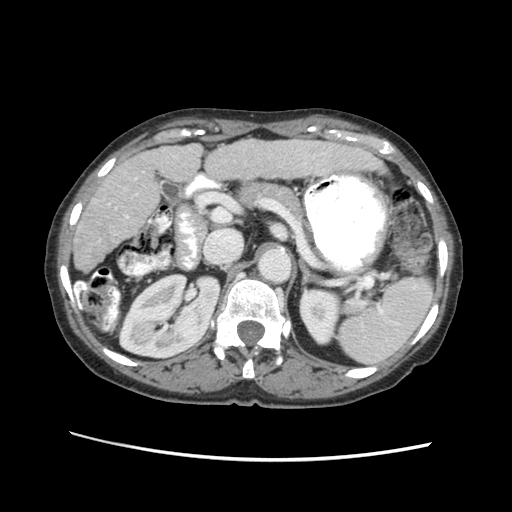
Contrast-enhanced abdominal CT (liver protocol), one axial slice; slice 28 of 63 in the series (ordered by position); 120 kVp; soft-tissue window (W 400 / L 40 HU); 512 × 512 image matrix, field of view 340 × 340 mm. From the clinical record (not read from this slice): diagnosis: hepatocellular carcinoma (patient treated with transarterial chemoembolisation; whether this scan precedes or follows treatment is not stated here); TNM stage (as recorded): Stage-I.
Annotated regions visible in this slice (semi-automatic segmentation, software-assisted and operator-edited):
- liver parenchyma outside the tumour (the mass and vessels are separate outlines, so this box may not span the whole liver): box from (x=72, y=134) to (x=390, y=270) px
- liver vessels: (x=133, y=148)–(x=302, y=193)